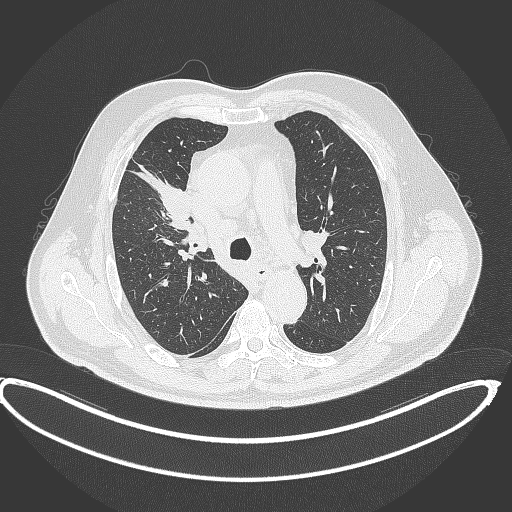
Chest CT, one axial slice; position 276 of 390 along the scan axis; lung window (W 1500 / L -600 HU); 1 mm slice thickness; 512 × 512 image matrix, field of view 448 × 448 mm. Male patient, age 62 years. Case-level facts recorded for this patient, not image findings: clinical TNM (as recorded): T1c N3 M1c.
Annotated regions visible in this slice (rectangle marked by the reading radiologist):
- lung tumour (recorded histology: adenocarcinoma): box from (x=154, y=179) to (x=193, y=224) px